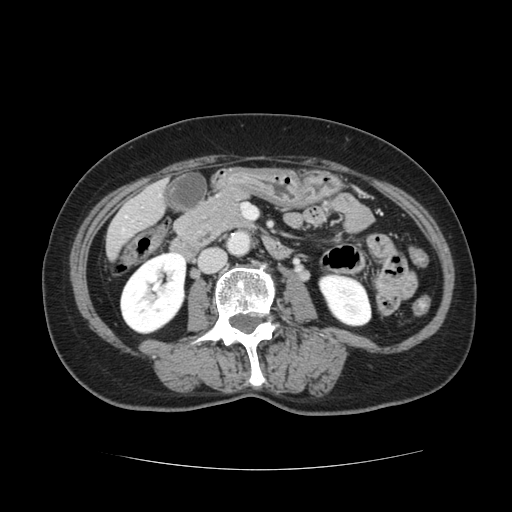
Contrast-enhanced abdominal CT, one axial slice. Slice 26 of 128 in the series (ordered by position). 120 kVp. Intravenous contrast given. Soft-tissue window (W 400 / L 40 HU). 512 × 512 image matrix, field of view 366 × 366 mm. Female patient, age 67 years. From the clinical record (not read from this slice): diagnosis: colorectal cancer liver metastases, imaged before liver resection; multiple liver metastases: yes; largest metastasis: 3 cm.
Structures marked on this image (outlined manually by an expert reader):
- liver: bounding box (x1, y1, x2, y2) in pixels: (107, 183, 165, 255)
- planned liver remnant (the part of the liver to remain after resection): (107, 210, 140, 256)